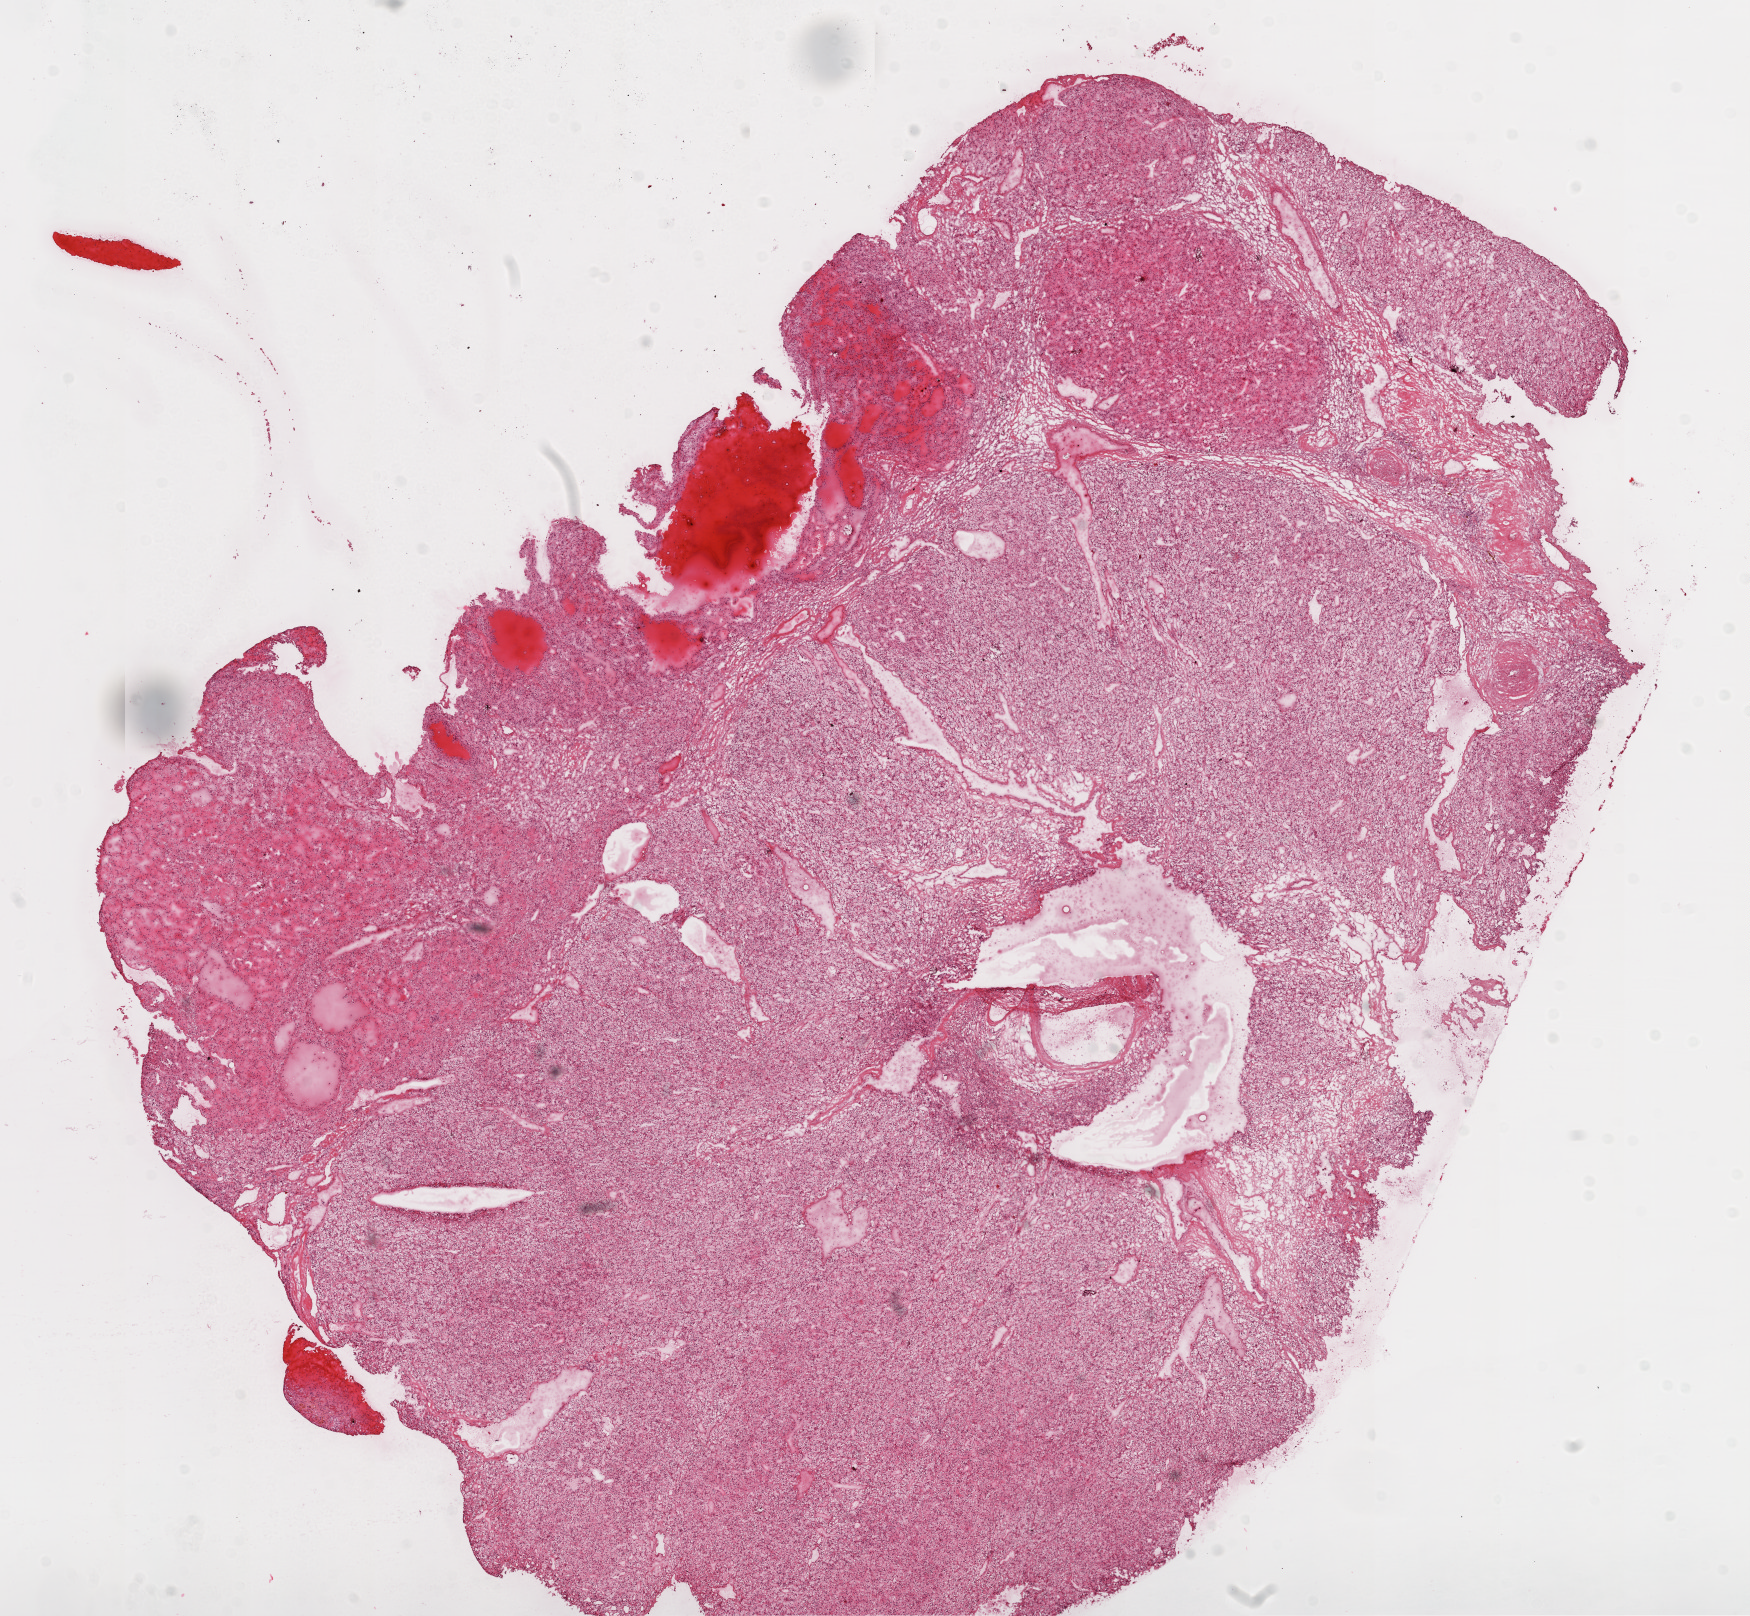
H&E whole-slide image, low-resolution overview of the scanned area, about 14.0 x 13.0 mm; frozen section from the top of the tissue portion; primary tumour sample from the kidney. Female, age 68 years at initial diagnosis. Histologic grade: G2 (moderately differentiated). Slide review estimates, as recorded: tumour cells 85%, tumour nuclei 85%, normal cells 0%, stromal cells 15%, necrosis 0%.
TNM: T1a NX M0. Histologic diagnosis: Clear cell adenocarcinoma, NOS. AJCC pathologic stage: I.